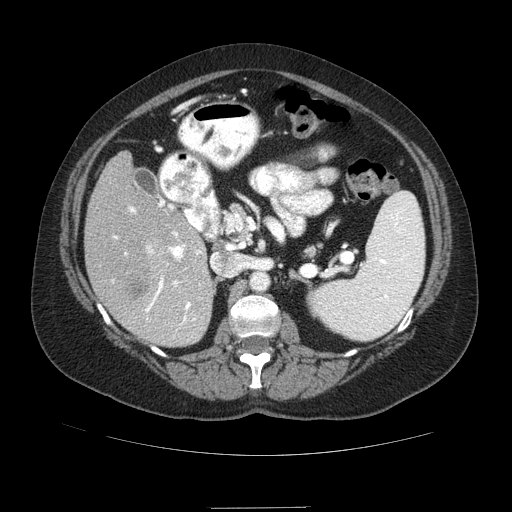
Contrast-enhanced abdominal CT (liver protocol), one axial slice; slice 41 of 89 in the series (ordered by position); 120 kVp; soft-tissue window (W 400 / L 40 HU); 2.5 mm slice thickness; 512 × 512 image matrix, field of view 400 × 400 mm. From the clinical record (not read from this slice): diagnosis: hepatocellular carcinoma (patient treated with transarterial chemoembolisation; whether this scan precedes or follows treatment is not stated here); TNM stage (as recorded): Stage-IIIB; Child-Pugh class: A; tumour nodularity: multinodular.
Structures marked on this image (semi-automatic segmentation, software-assisted and operator-edited):
- liver parenchyma outside the tumour (the mass and vessels are separate outlines, so this box may not span the whole liver): bounding box <84,152,214,346> (left, top, right, bottom; pixels)
- mass: <123,280,148,299>
- liver vessels: <112,199,201,327>